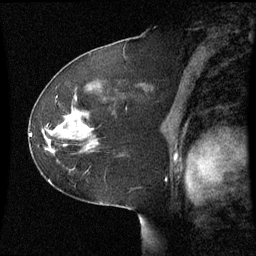
Breast MRI (dynamic contrast-enhanced), one sagittal slice. Slice 38 of 60 in the series (ordered by position). Dynamic contrast-enhanced series, image 2 of 3 at this slice position (ordered by acquisition). 1.5 T. TE 4.2 ms, TR 8.9 ms. 2.2 mm slice thickness. 256 × 256 image matrix, field of view 220 × 220 mm. Patient: female, 51 years. Case-level facts recorded for this patient, not image findings: setting: breast cancer imaged before/during neoadjuvant chemotherapy; receptor status: HR-positive, HER2-negative.
Structures marked on this image (semi-automatic segmentation, software-assisted and operator-edited):
- analysis volume of interest (the breast-tissue region the enhancement analysis was run in; not a lesion): bounding box <44,104,101,169> (left, top, right, bottom; pixels)
- tumour enhancement mask (voxels above the 70 % enhancement threshold inside the analysis volume of interest): <76,114,87,129>